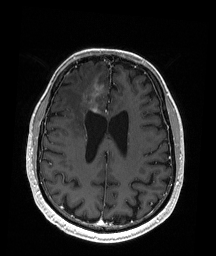
Brain MRI from a brain-tumour surgery series, one axial slice; slice 72 of 192 in the series (ordered by position); T1-weighted post-contrast; 1 mm slice thickness; 216 × 256 image matrix, field of view 211 × 250 mm. From the clinical record (not read from this slice): histopathology: Astrocytoma; WHO grade: 3; IDH mutation: yes.
Outlined on this slice (manually delineated by an expert):
- tumour: bounding box [x1, y1, x2, y2] px = [86, 93, 99, 113]